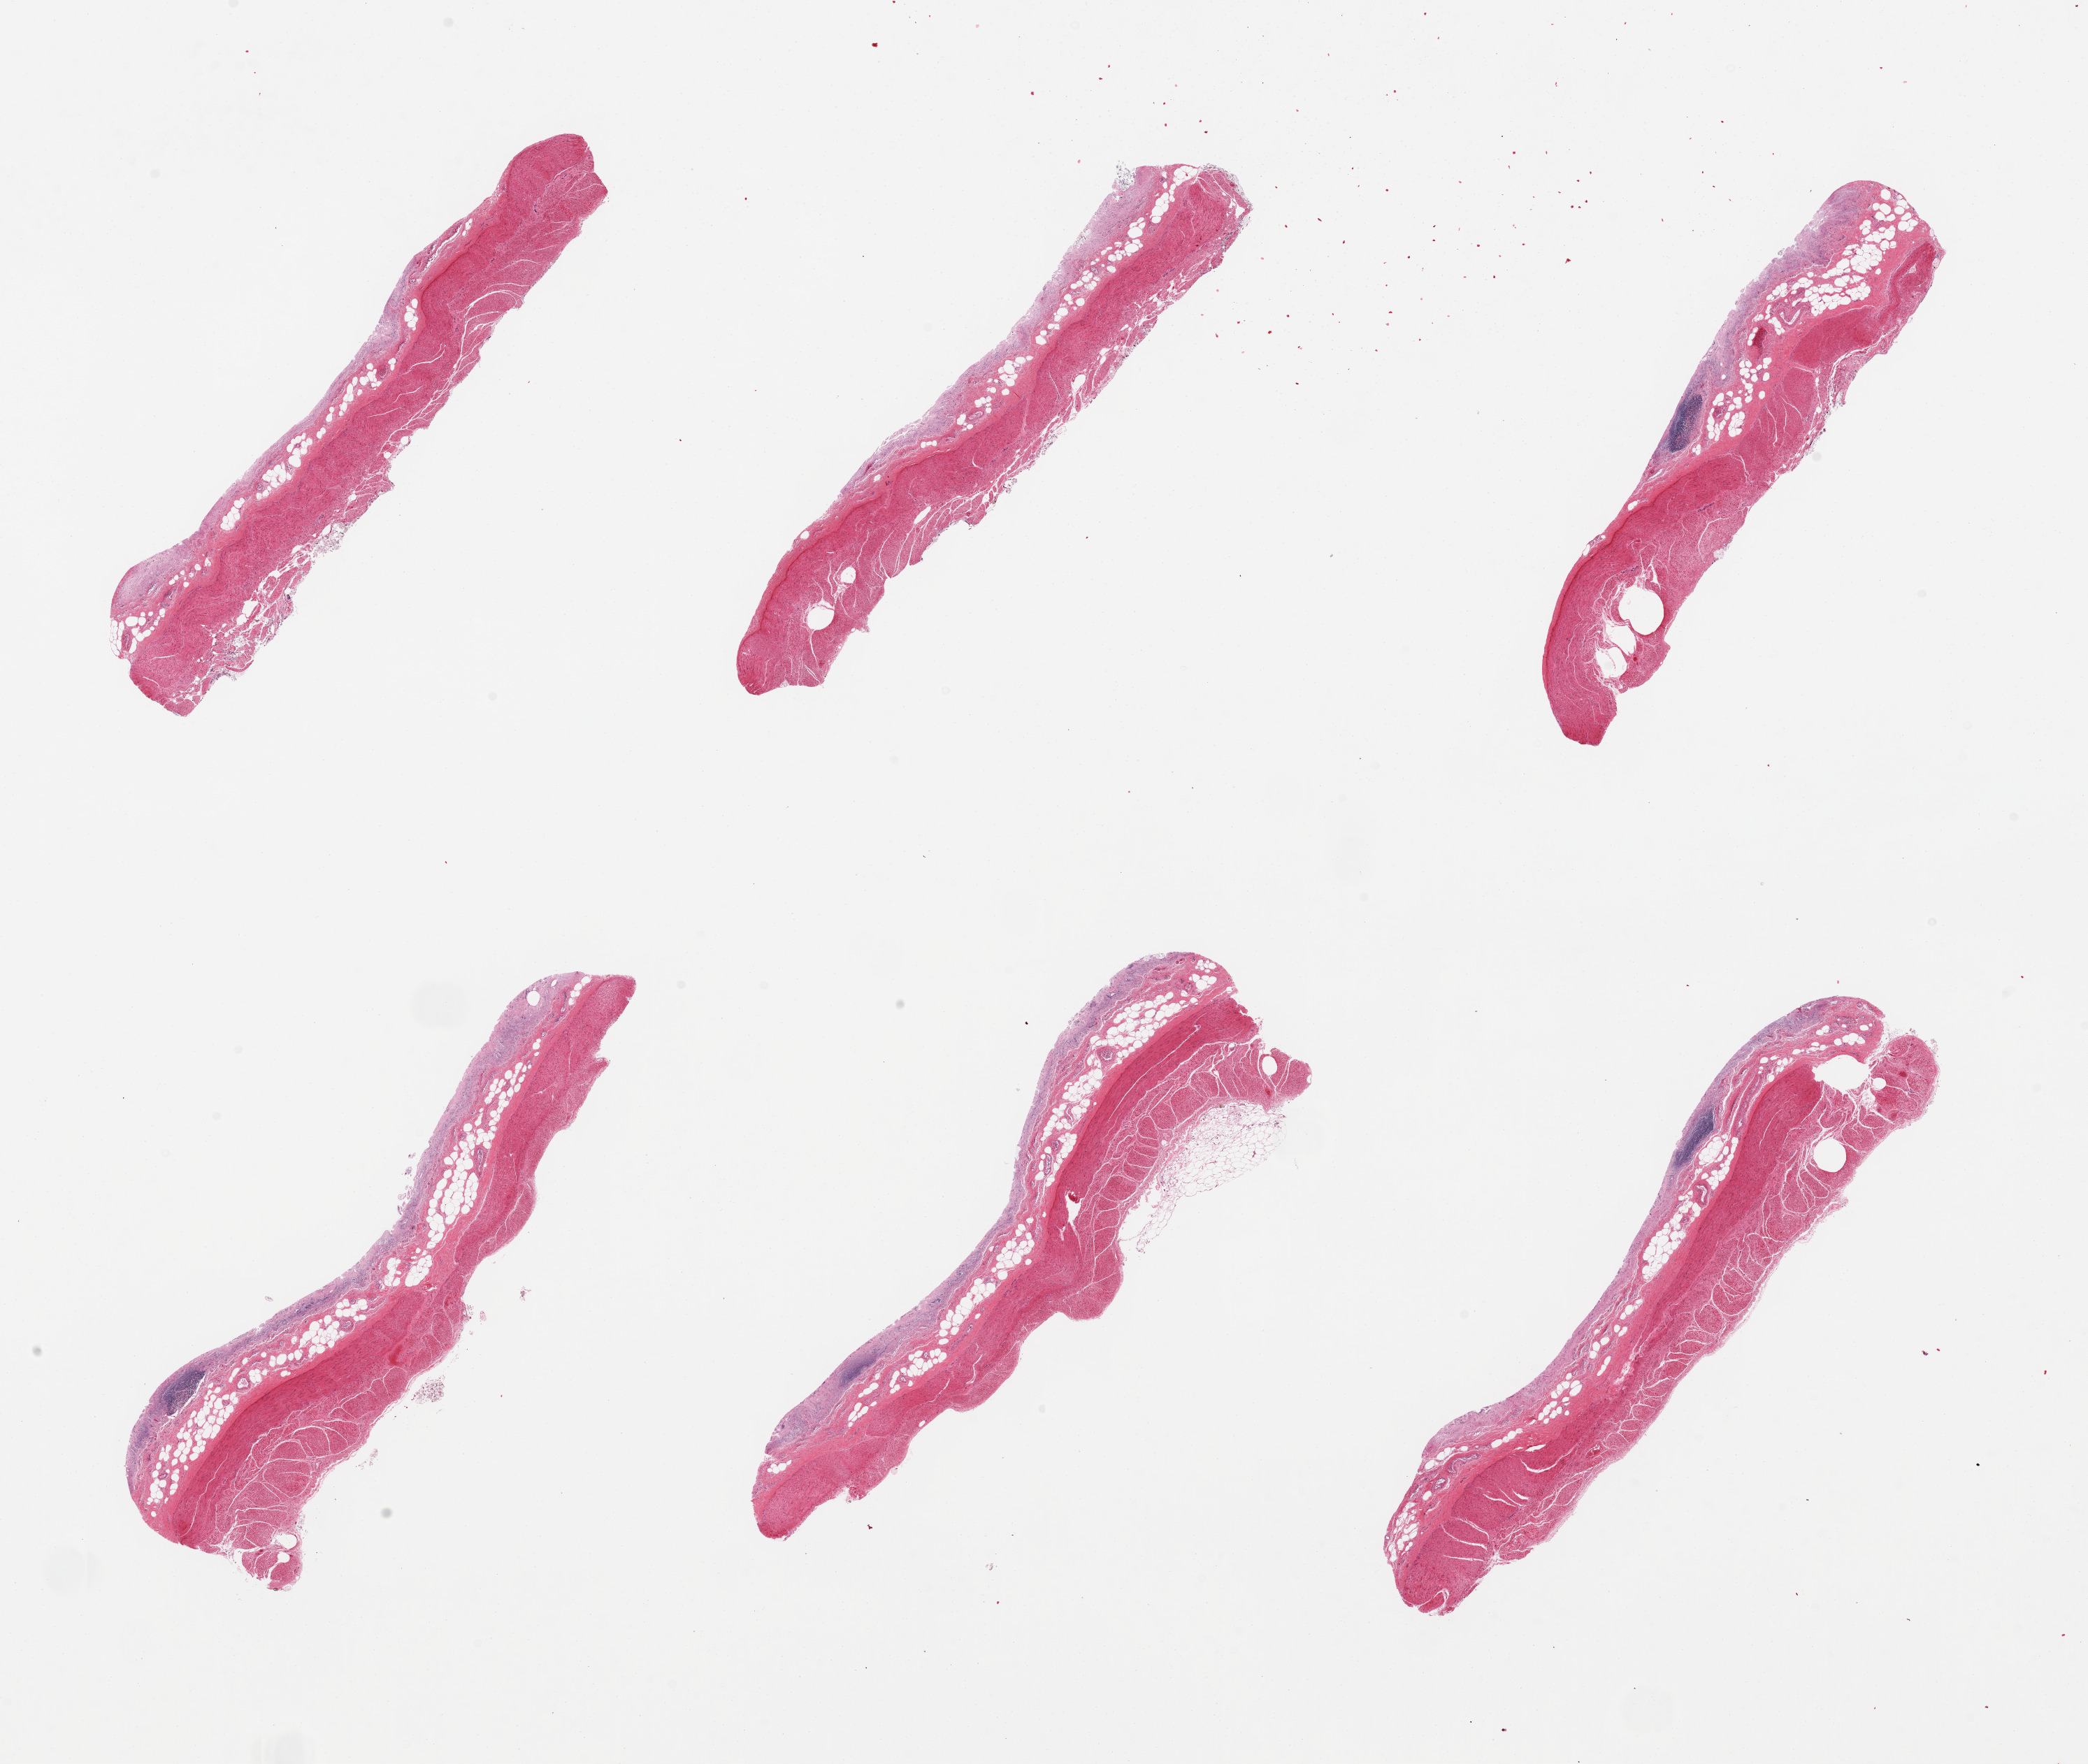
Whole-slide image, H&E stain, brightfield — a low-resolution overview of the entire scanned area, about 23.6 x 20.0 mm (acquisition: 20x scan). PAXgene-fixed paraffin-embedded (PFPE) section. Sampled site (target tissue): ileum. Tissue donor sample. Donor sex: male.
• pathologist's review note for this sample: 6 pieces; mucosa totally autolyzed, small lymphoid foci largely autolyzed